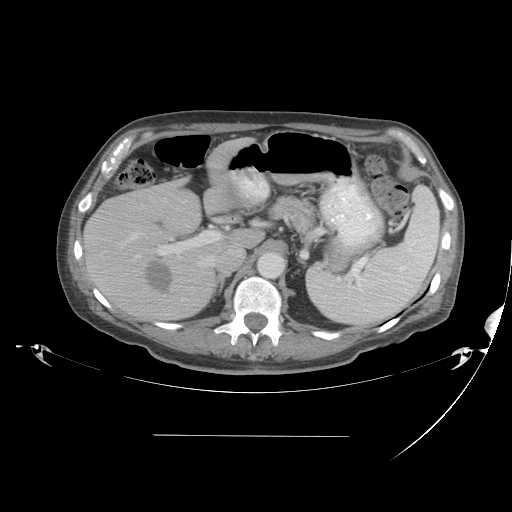
Contrast-enhanced abdominal CT, one axial slice. Position 27 of 48 along the scan axis. 120 kVp. Soft-tissue window (W 400 / L 40 HU). 512 × 512 image matrix, field of view 486 × 486 mm. Male patient, age 65 years. Case-level facts recorded for this patient, not image findings: diagnosis: colorectal cancer liver metastases, imaged before liver resection; multiple liver metastases: yes; largest metastasis: 11 cm; disease in both lobes: yes.
Annotated regions visible in this slice (expert manual segmentation):
- hepatic veins: bounding box <118,231,211,302> (left, top, right, bottom; pixels)
- liver: <84,139,254,320>
- planned liver remnant (the part of the liver to remain after resection): <146,139,257,244>
- portal vein (with intrahepatic branches): <137,226,225,257>
- liver metastasis: <143,259,174,292>